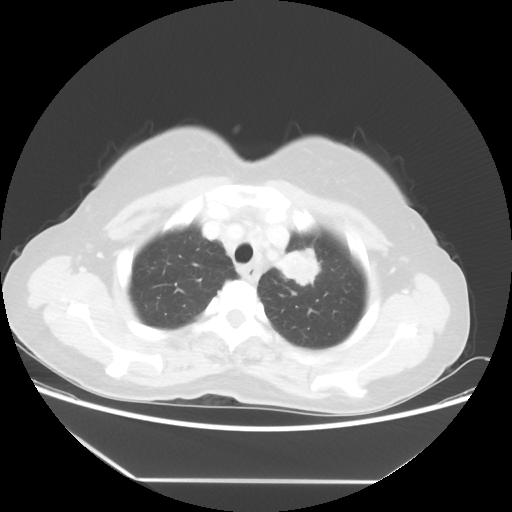
Chest CT, one axial slice. Position 44 of 52 along the scan axis. Lung window (W 1500 / L -600 HU). 512 × 512 image matrix, field of view 390 × 390 mm. Patient: female, 50 years. Case-level facts recorded for this patient, not image findings: clinical TNM (as recorded): T2 N3 M0.
Outlined on this slice (bounding box drawn by a radiologist):
- lung tumour (recorded histology: adenocarcinoma): bounding box (x1, y1, x2, y2) in pixels: (266, 235, 323, 300)